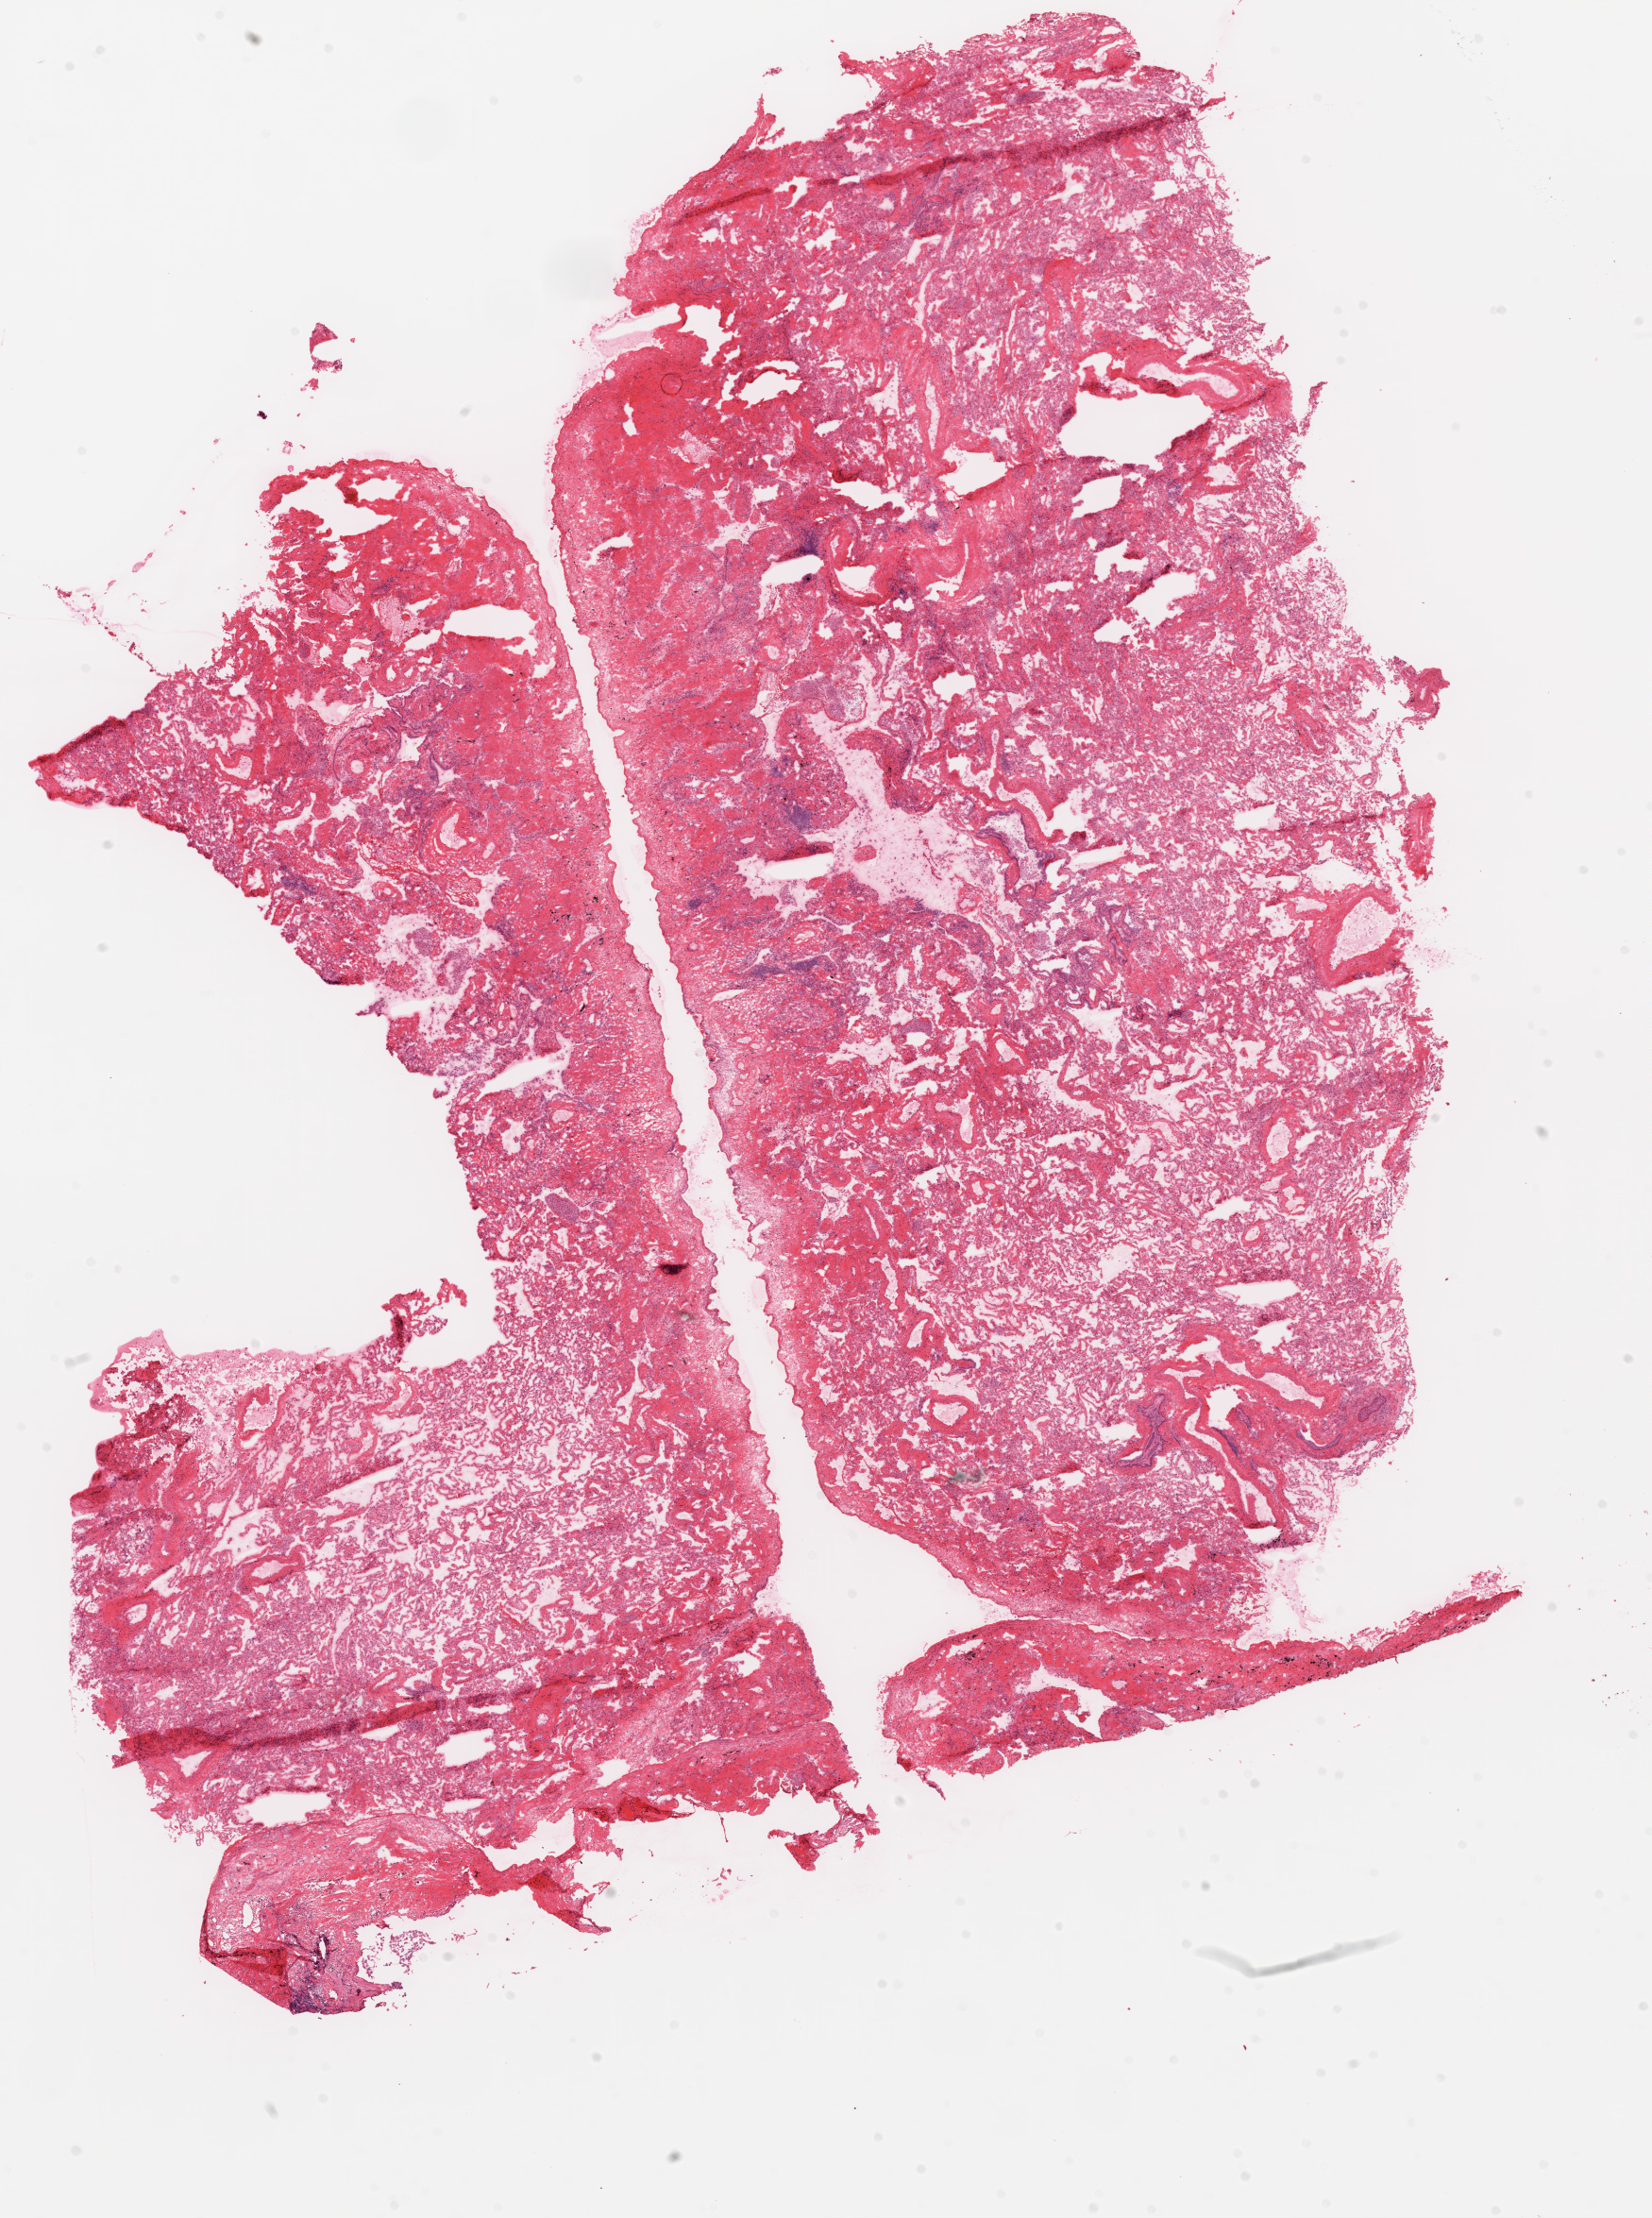
H&E whole-slide image — low-resolution overview of the scanned area, about 14.0 x 18.8 mm (from a 20x scan). Frozen section from the top of the tissue portion. Solid tissue normal (non-tumour tissue) sample from the lung. Female, age 72 years at initial diagnosis.
This section: solid tissue normal sample (biorepository sample class). Patient diagnosis: Squamous cell carcinoma, NOS.